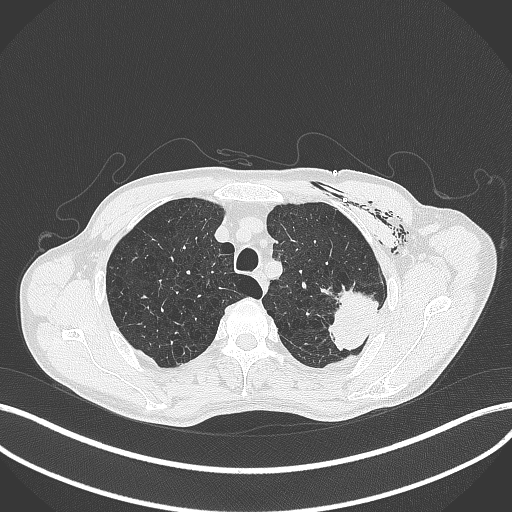
Chest CT, one axial slice. Position 333 of 457 along the scan axis. 120 kVp. Lung window (W 1500 / L -600 HU). 512 × 512 image matrix, field of view 400 × 400 mm. Male patient, age 58 years. Case-level facts recorded for this patient, not image findings: clinical TNM (as recorded): T3 N0 M0.
Structures marked on this image (rectangle marked by the reading radiologist):
- lung tumour (recorded histology: adenocarcinoma): bounding box [x1, y1, x2, y2] px = [314, 280, 376, 352]